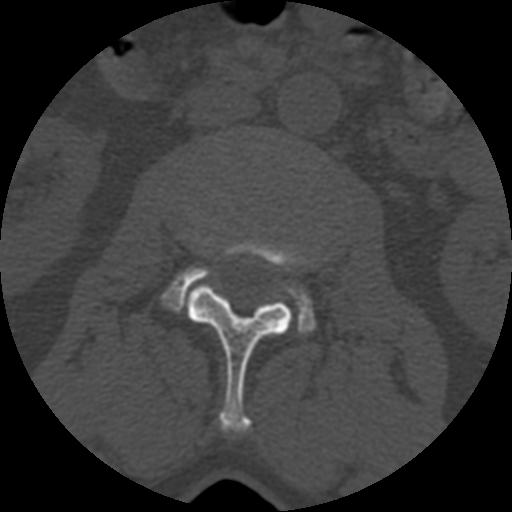
CT including the spine, one axial slice. Slice 325 of 399 in the series (ordered by position). 120 kVp. Bone window (W 1800 / L 400 HU). 1.25 mm slice thickness. 512 × 512 image matrix, field of view 160 × 160 mm. Patient age 71 years. From the clinical record (not read from this slice): primary cancer: prostate.
Annotated regions visible in this slice (semi-automatically segmented with operator editing):
- L2 vertebra: box from (x=185, y=240) to (x=294, y=433) px
- L3 vertebra: (x=160, y=266)–(x=315, y=333)